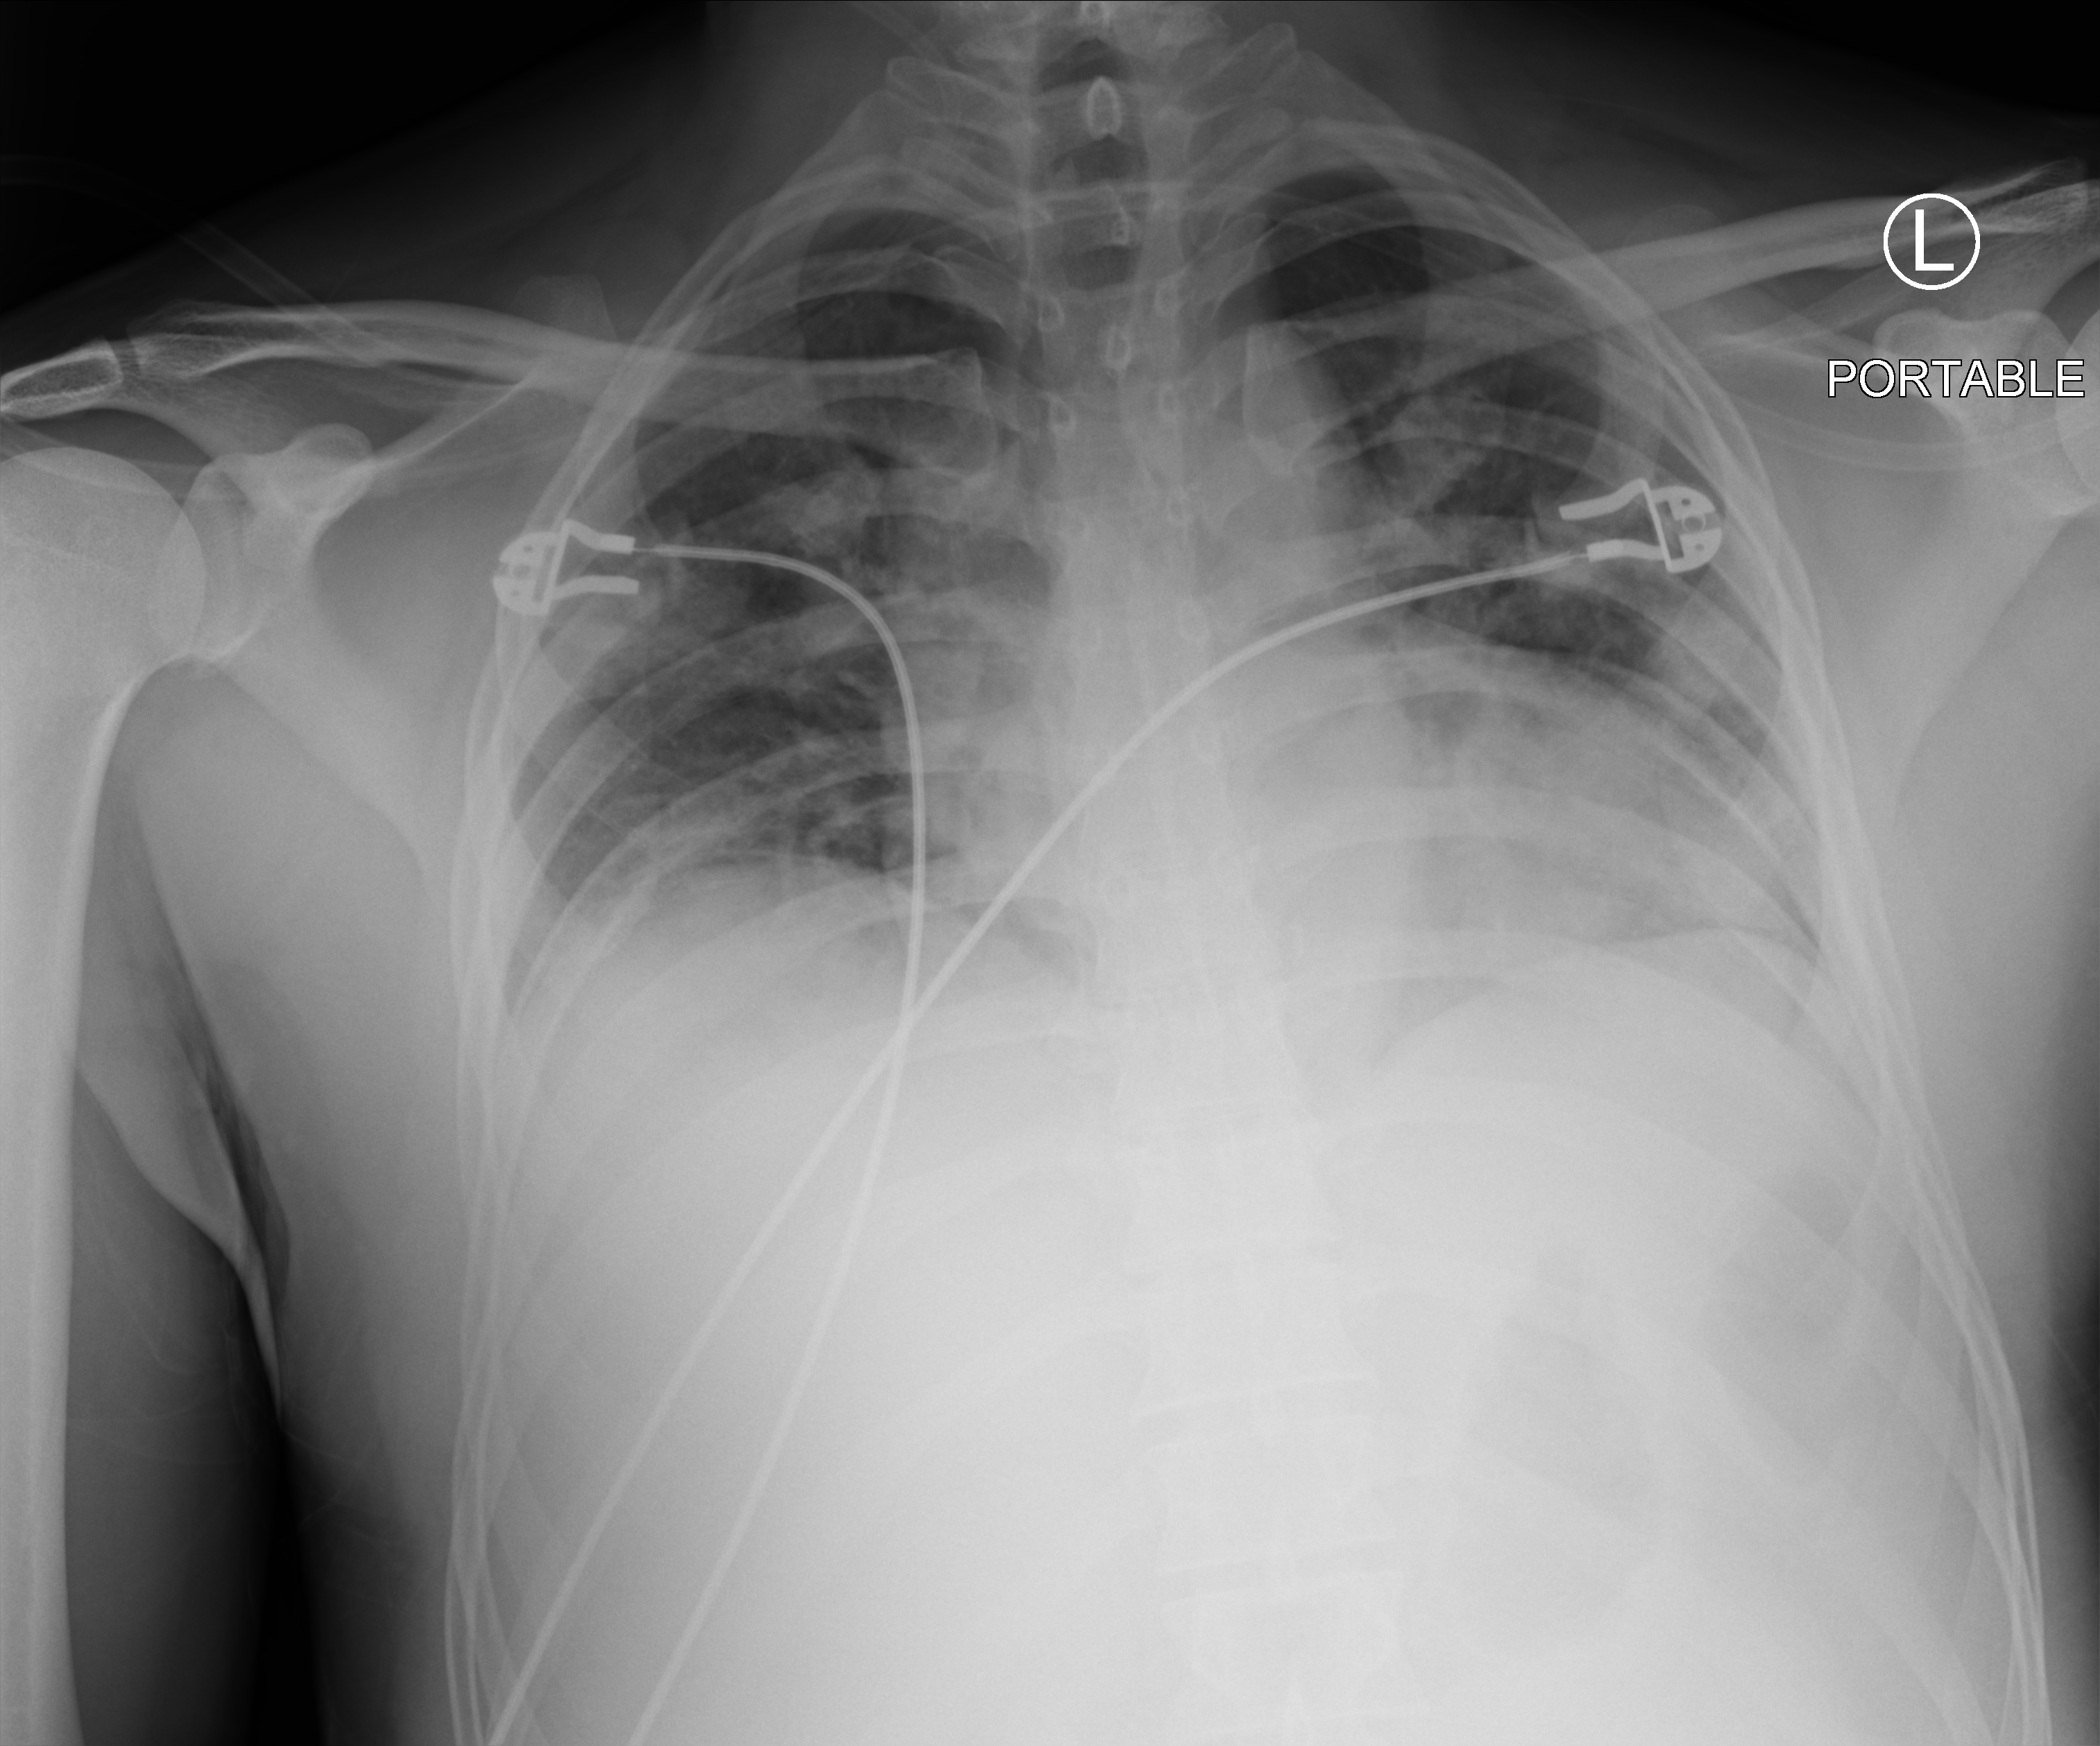
Bedside chest radiograph (computed radiography); anteroposterior (AP) projection. Male patient hospitalised with COVID-19, age 18–59 years.
Hospital-stay facts (about this admission, not read from this image; timing relative to this image not recorded): mechanically ventilated during this hospital stay: no; admitted to intensive care during this hospital stay: no.